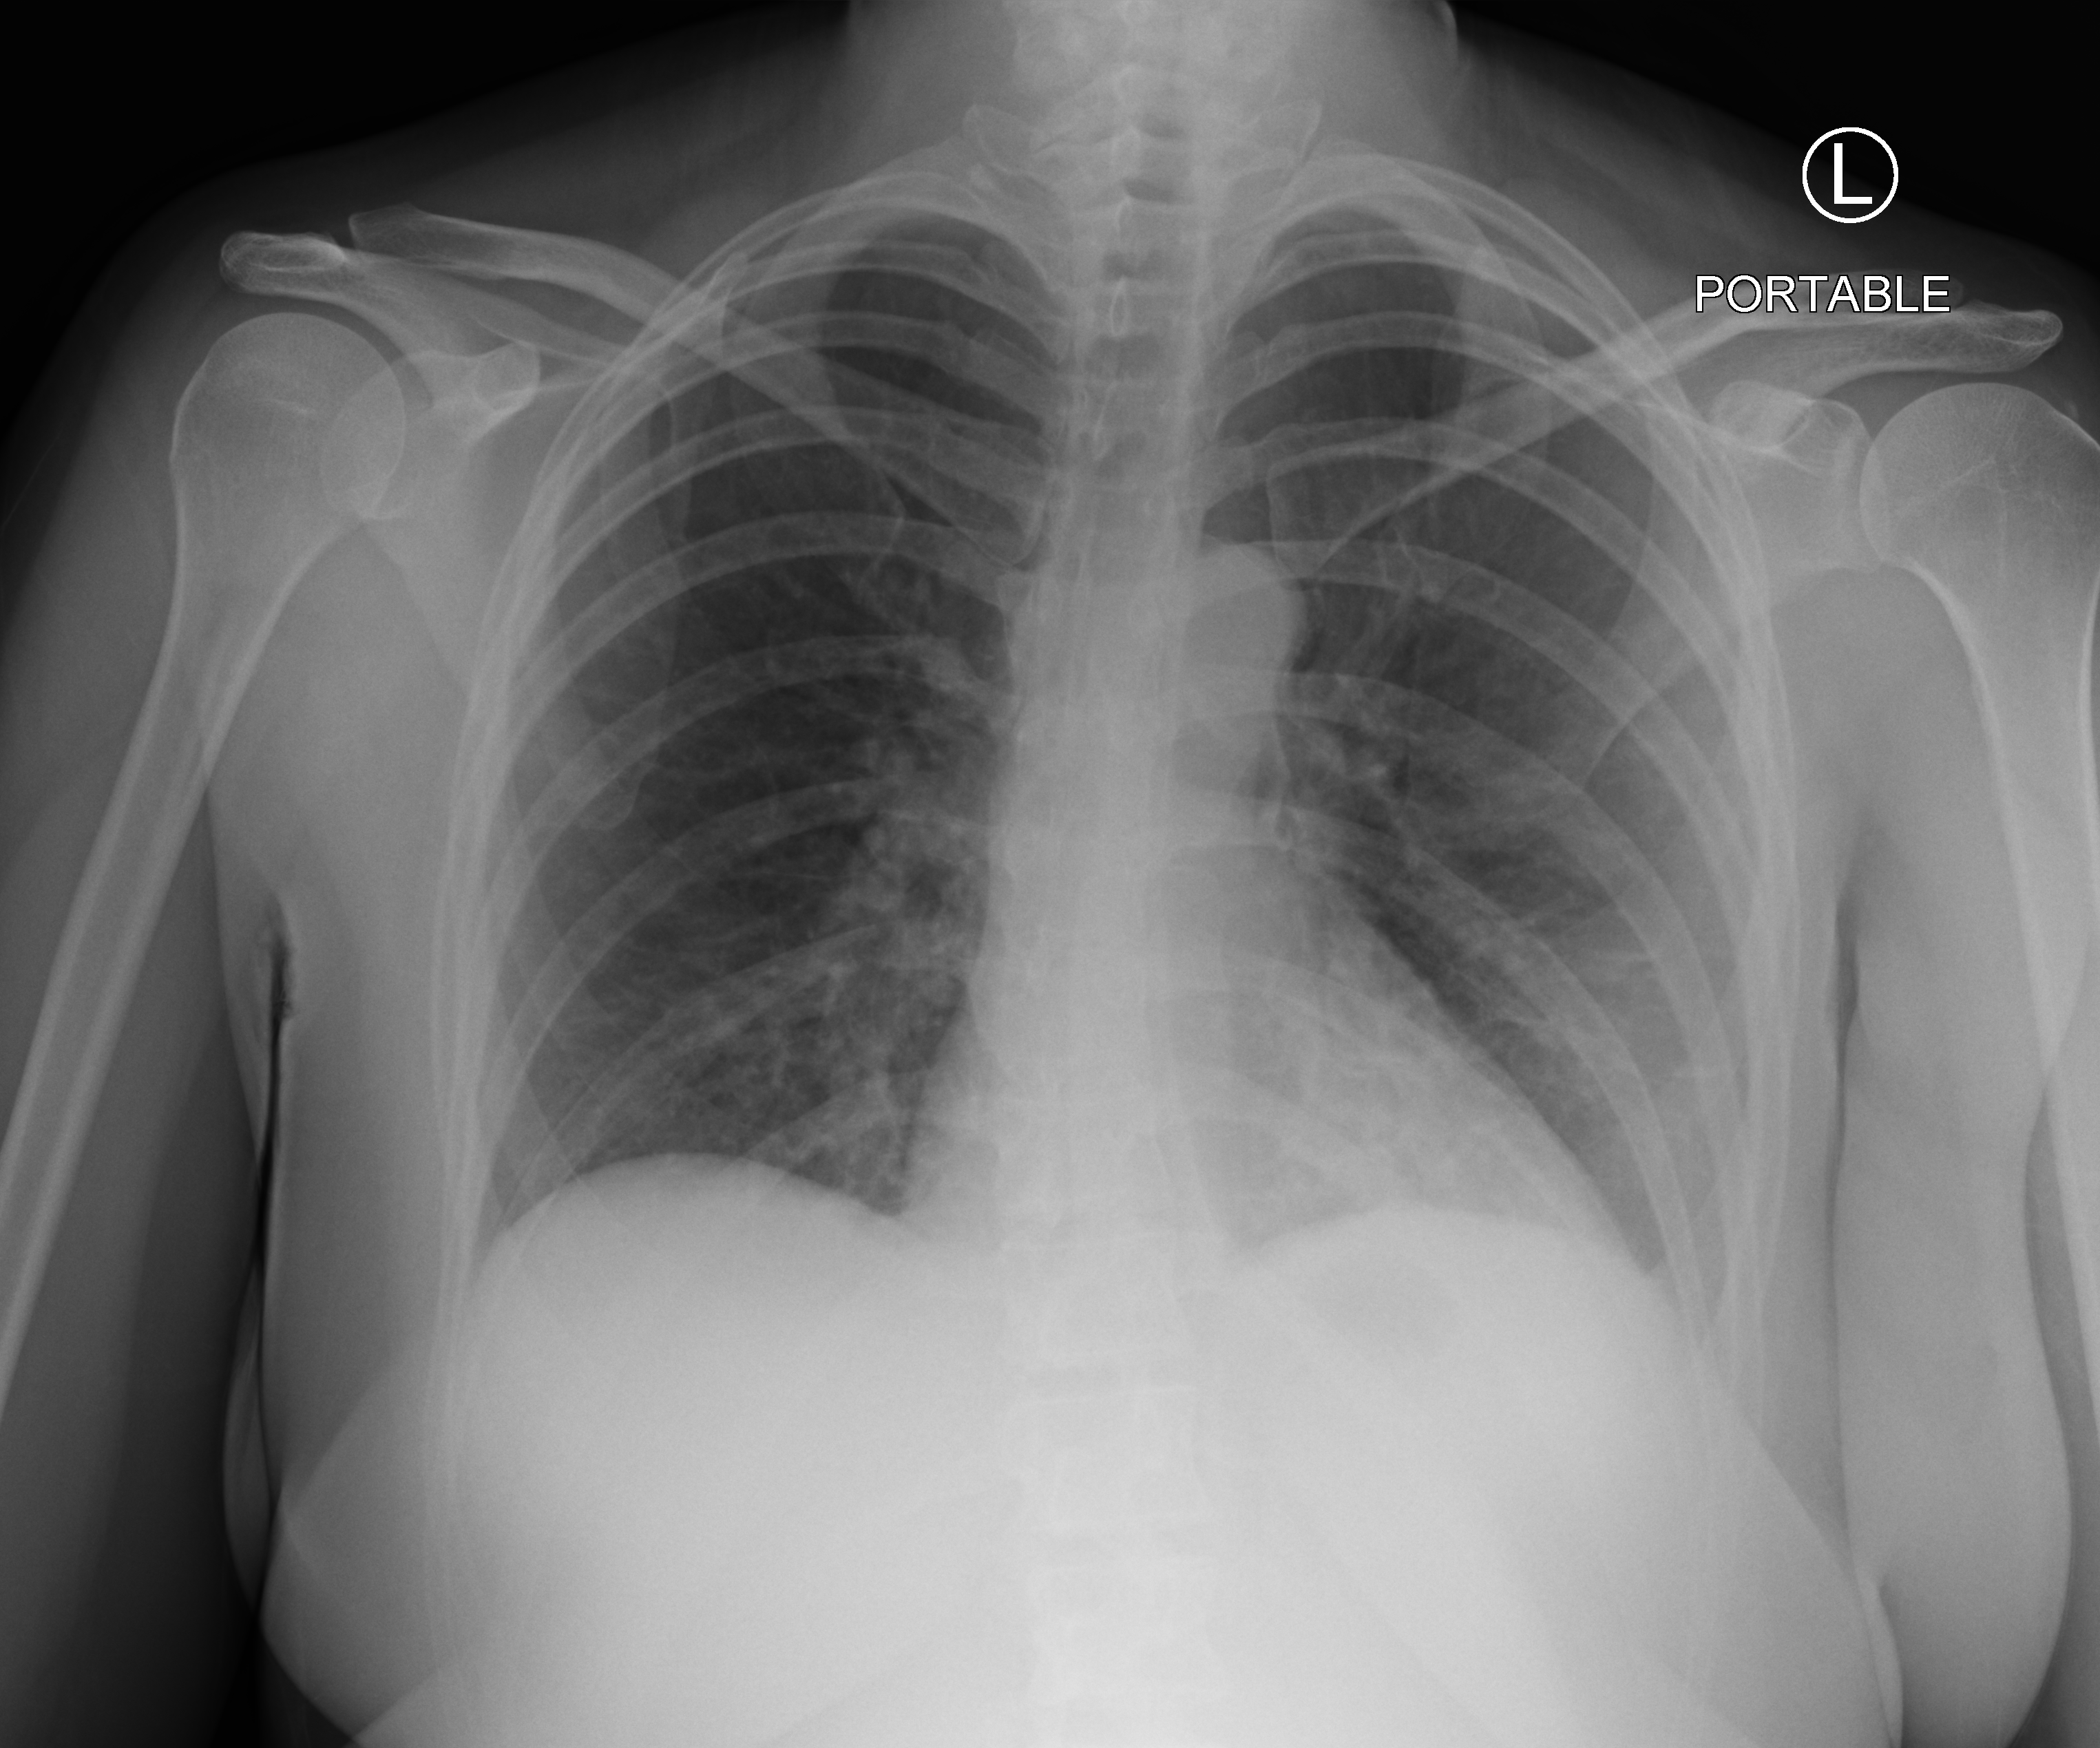
Chest X-ray (portable), anteroposterior (AP) projection. Female patient hospitalised with COVID-19, age 18–59 years.
From the hospital-stay record, not from the radiograph (when in the stay this image was taken is not recorded):
- mechanically ventilated during this hospital stay: no
- chronic kidney disease (admission record): no